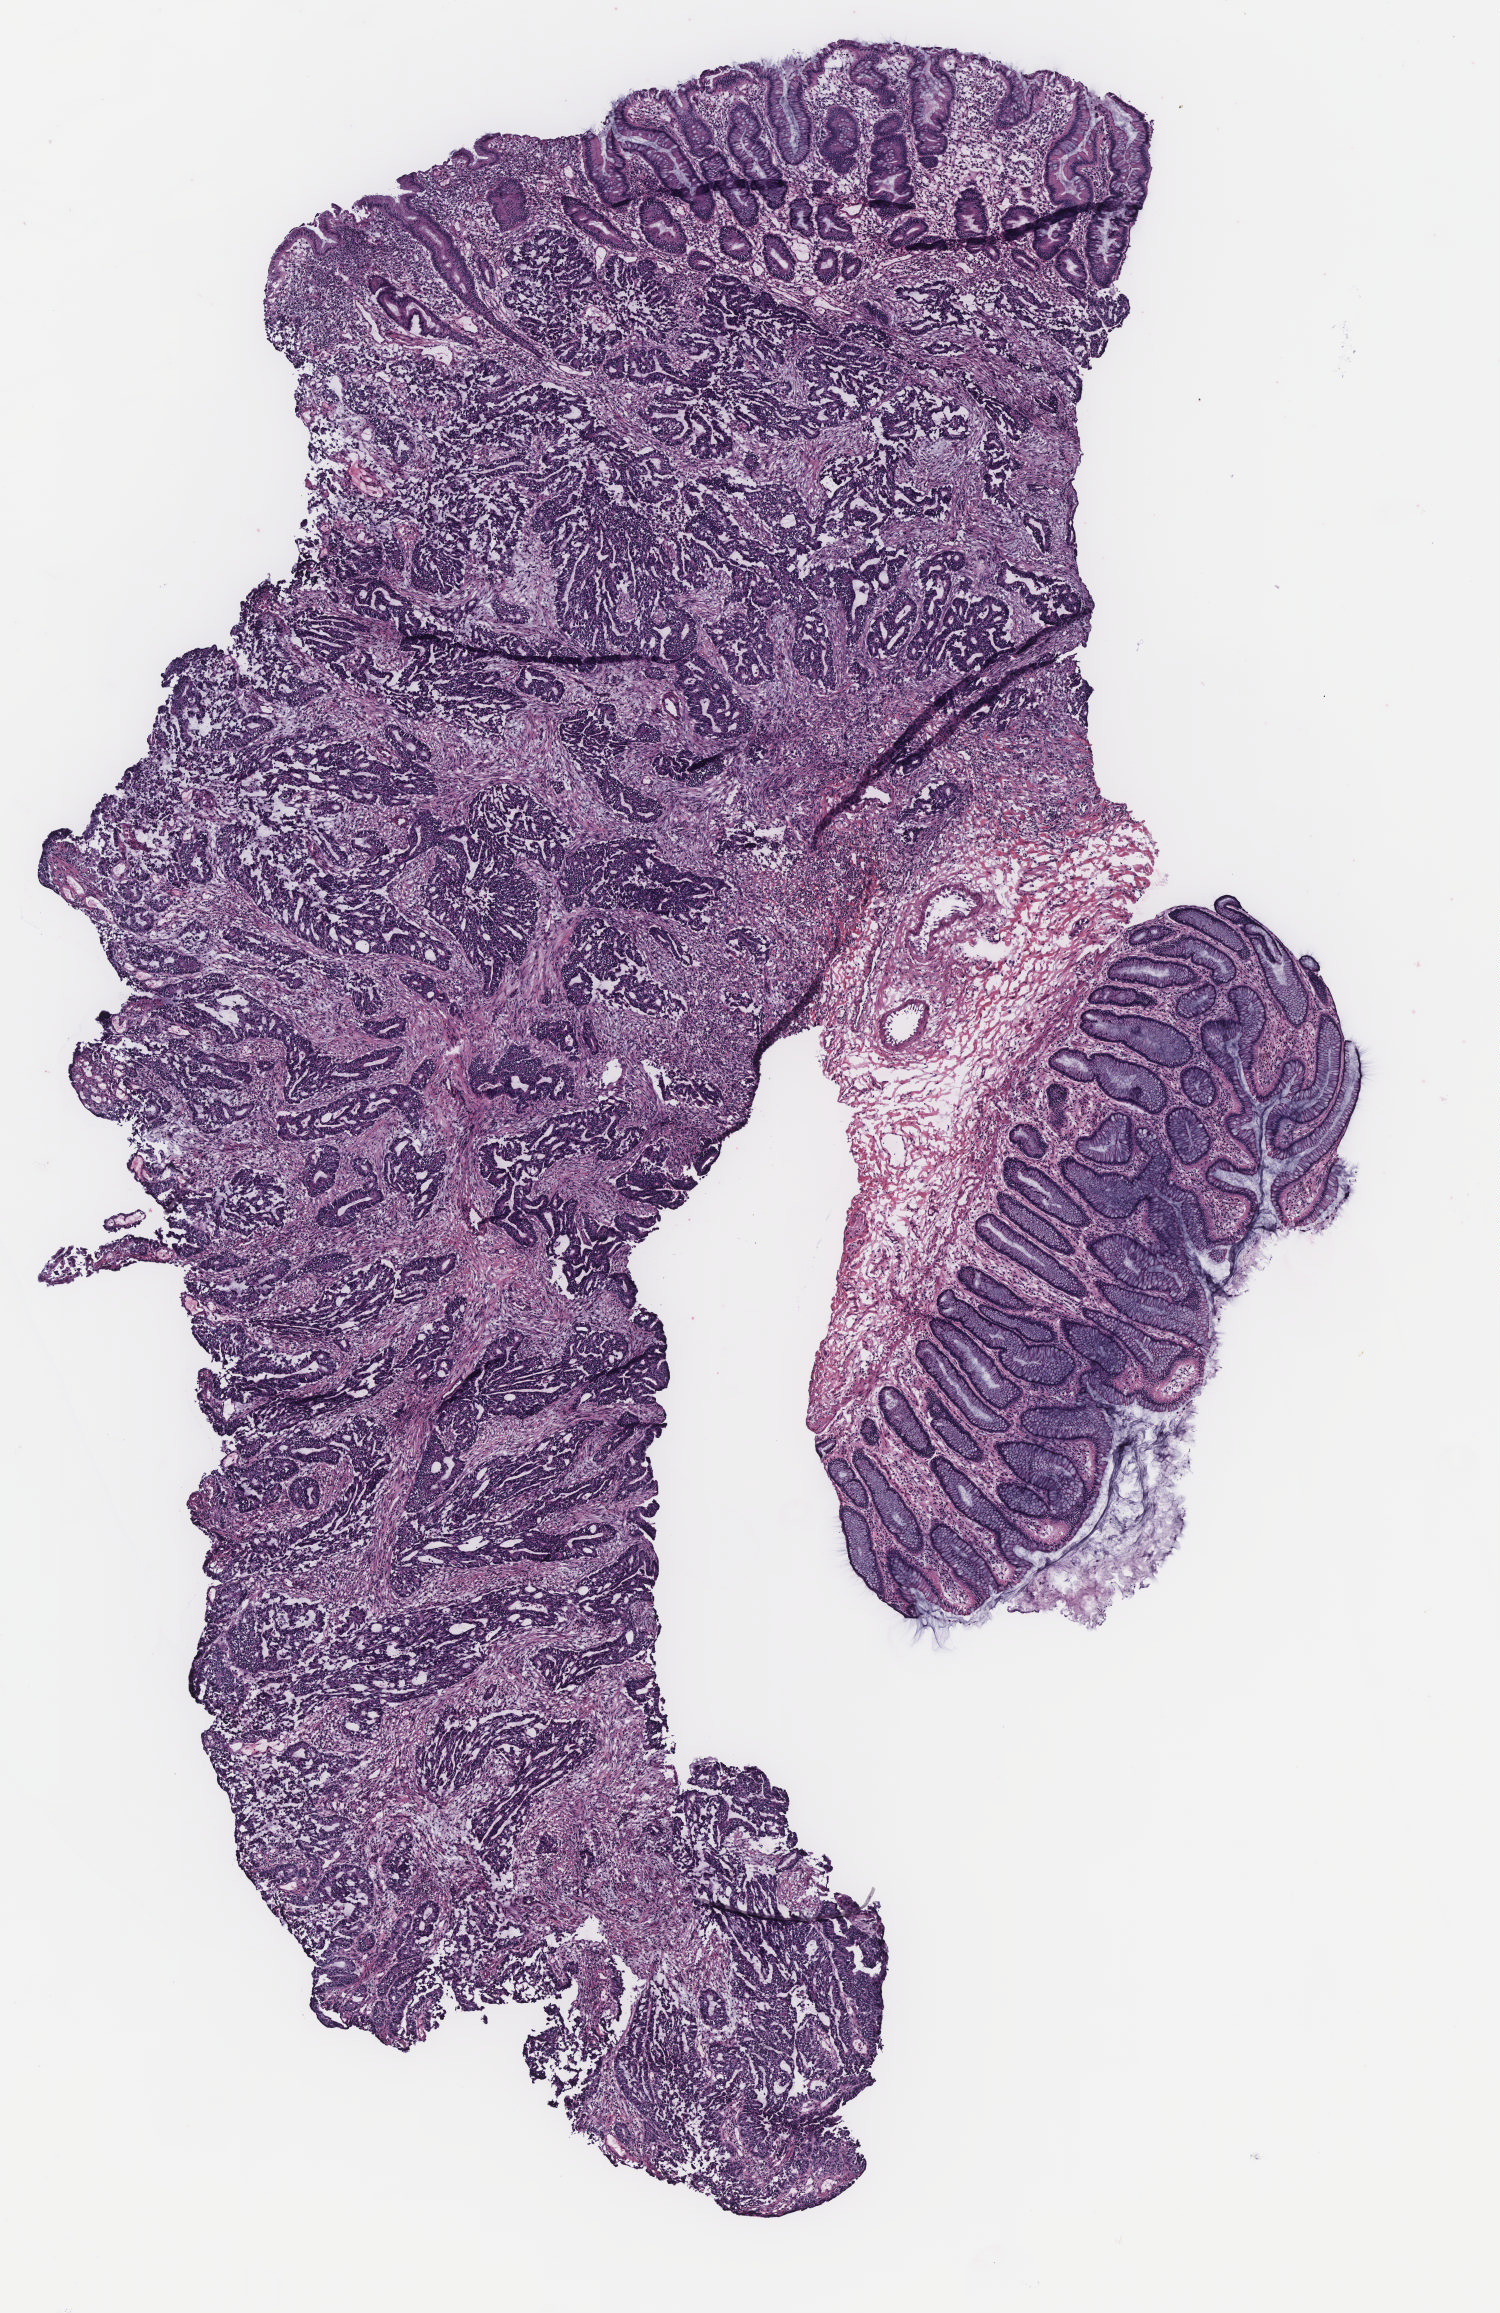
Digitized Hematoxylin and eosin (H&E) stained tissue section (whole slide), low-resolution overview of the scanned area, about 6.0 x 9.3 mm (from a 40x scan), colon, tissue type not recorded.
Patient diagnosis (cohort enrolment): colon cancer (colon).